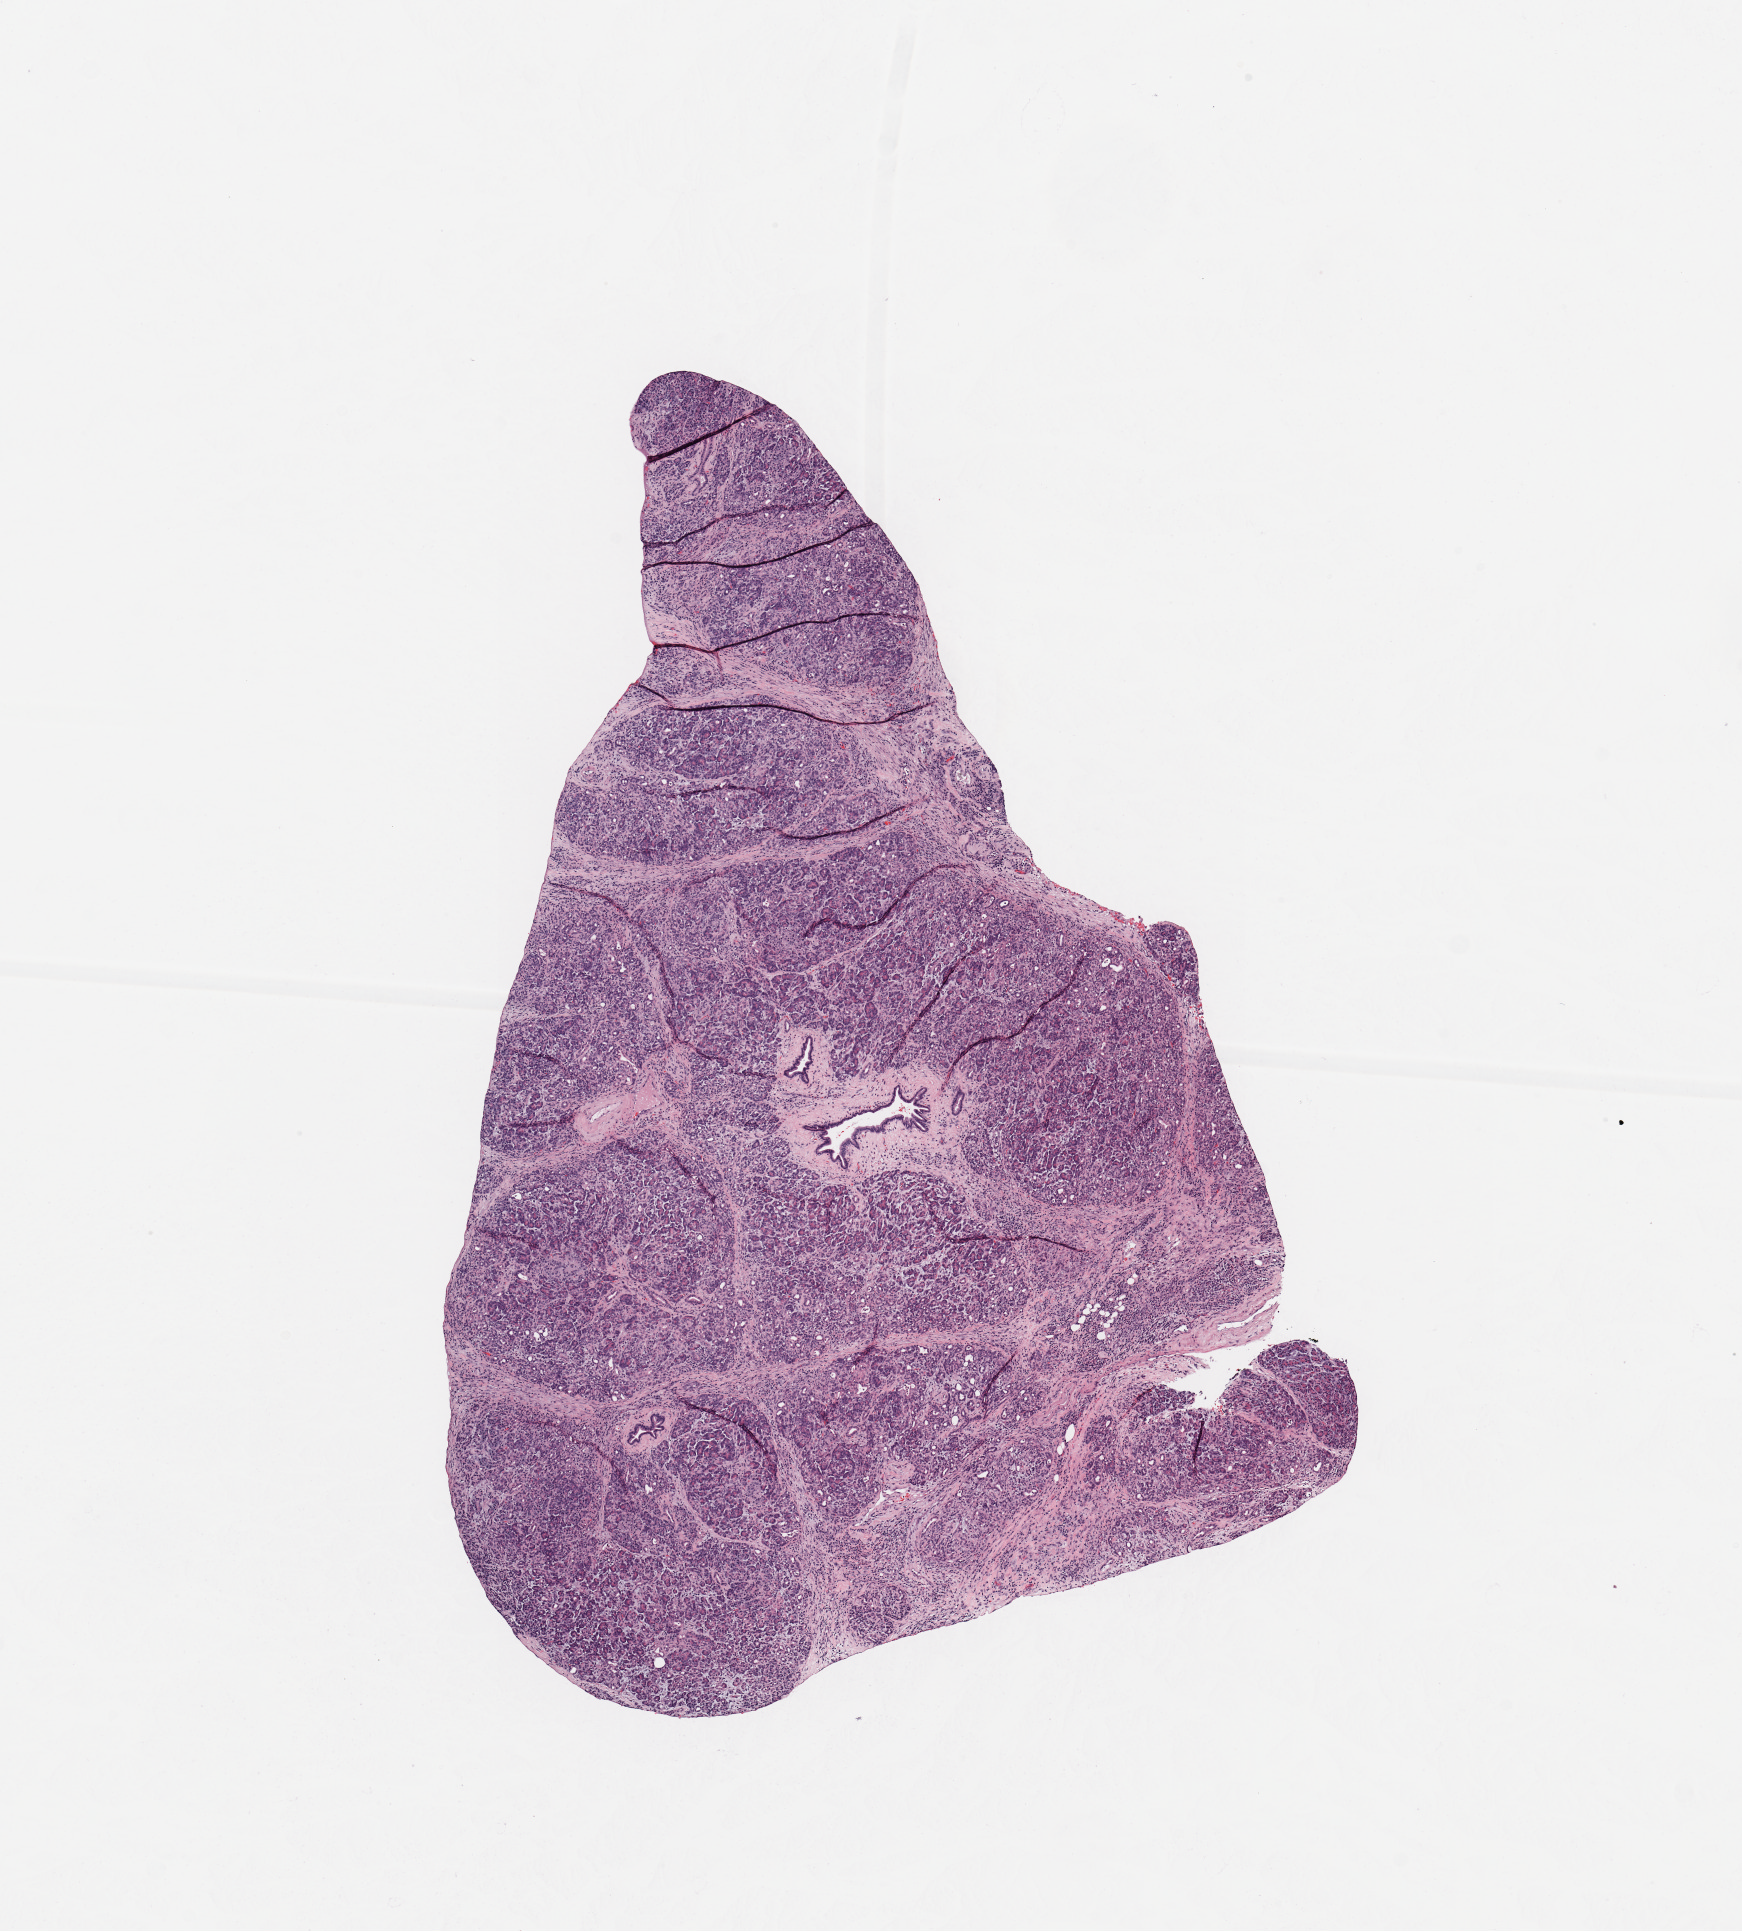
H&E whole-slide image, a low-resolution overview of the entire scanned area, about 6.9 x 7.6 mm (slide scanned at 20x). Normal (non-tumour) tissue sample, sampled site: pancreas. Patient: male, age 55 years.
This section: normal (non-tumour) tissue from the same patient. Patient diagnosis: Infiltrating duct carcinoma, NOS.